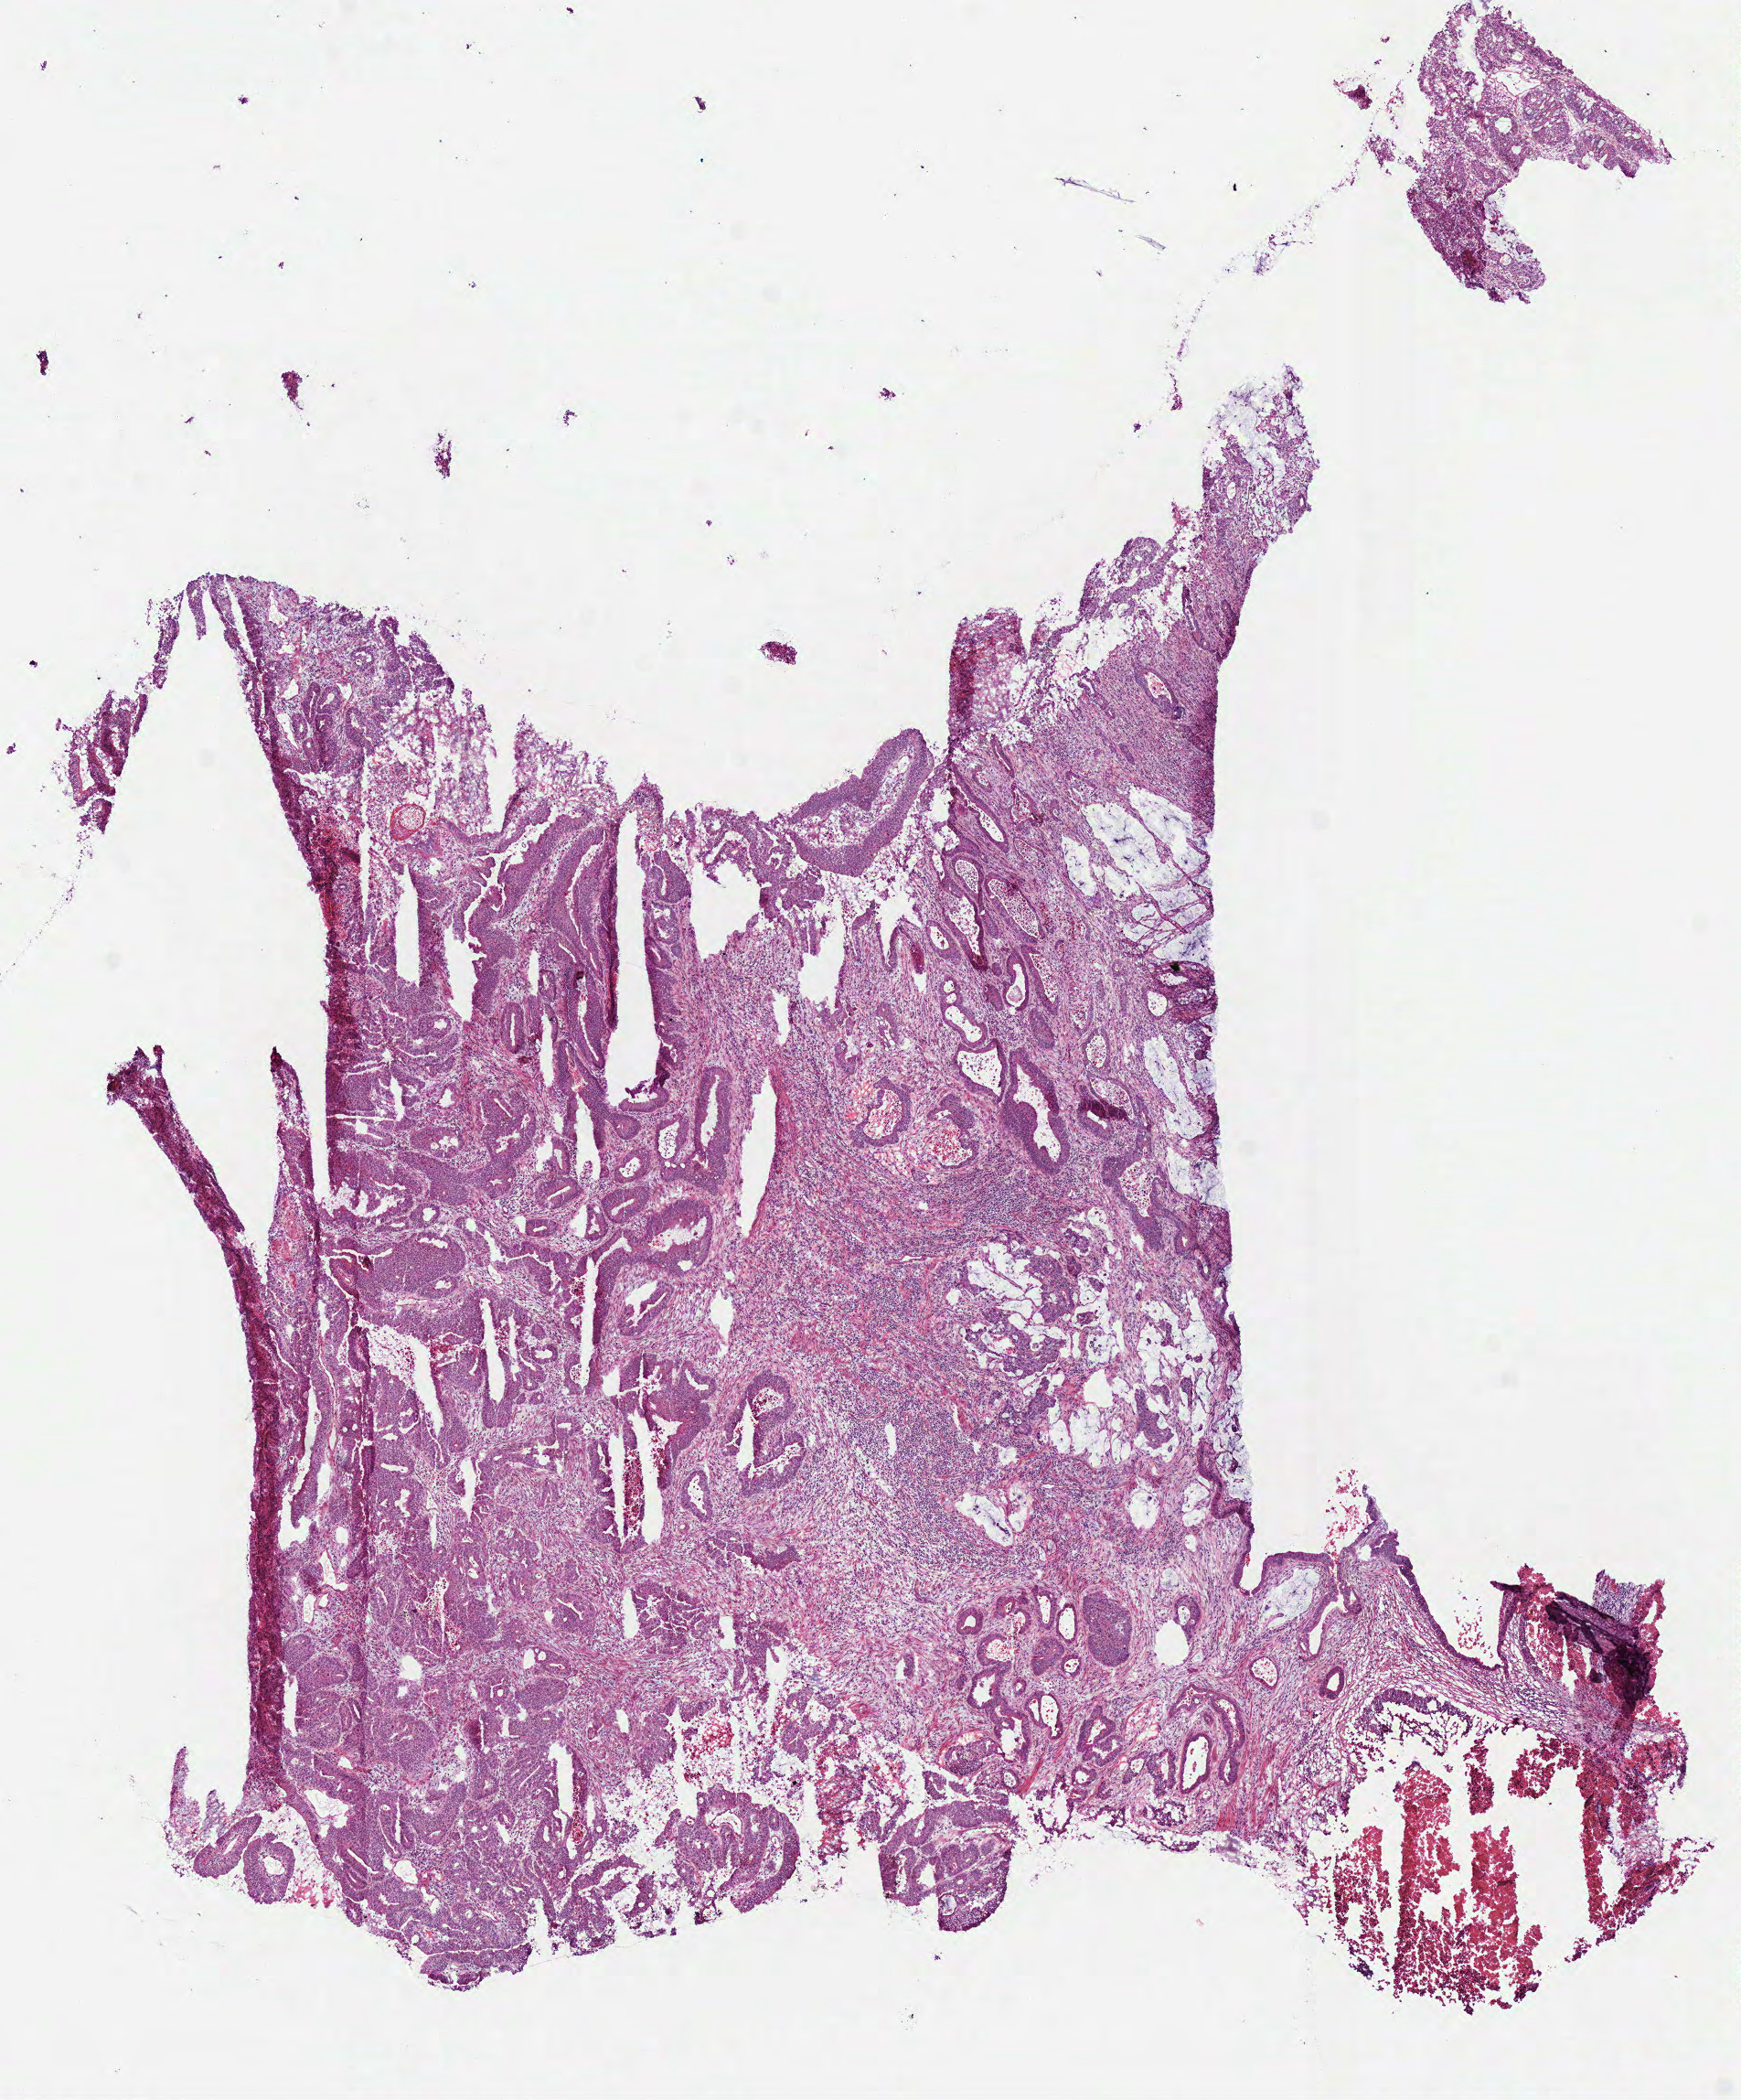
Whole-slide histology image, H&E-stained — low-resolution overview of the scanned area, about 7.5 x 9.0 mm, frozen section from the bottom of the tissue portion, primary tumour sample from the colon. Patient: male, age at initial diagnosis 84 years. Slide review estimates, as recorded: tumour cells 67%, tumour nuclei 55%, normal cells 0%, stromal cells 25%, necrosis 8%.
• AJCC pathologic stage: IIIC (7th edition)
• pathologic diagnosis: Mucinous adenocarcinoma
• TNM: T4a N2b MX